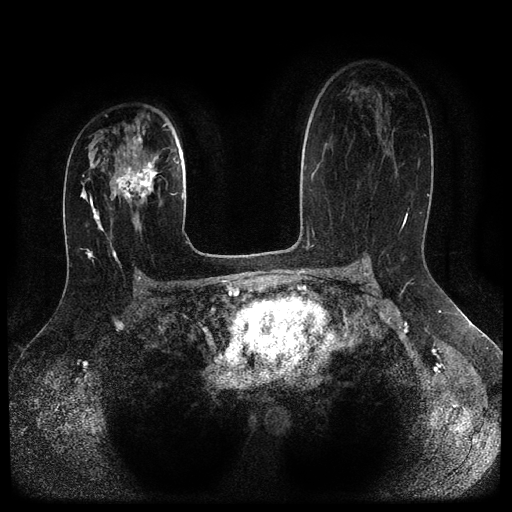
Breast MRI (dynamic contrast-enhanced, multi-phase), one axial slice. Position 64 of 116 along the scan axis. Dynamic contrast-enhanced series, time point 2 of 5 at this slice position (early post-contrast). 1.5 T. TE 2.6 ms, TR 5.4 ms. 512 × 512 image matrix. Patient: female, 29 years.
Structures marked on this image (semi-automatically segmented with operator editing):
- breast lesion (labelled 'tumour' in the annotation; benign lesions carry a separate 'benign' label): bounding box (x1, y1, x2, y2) in pixels: (110, 152, 163, 207)